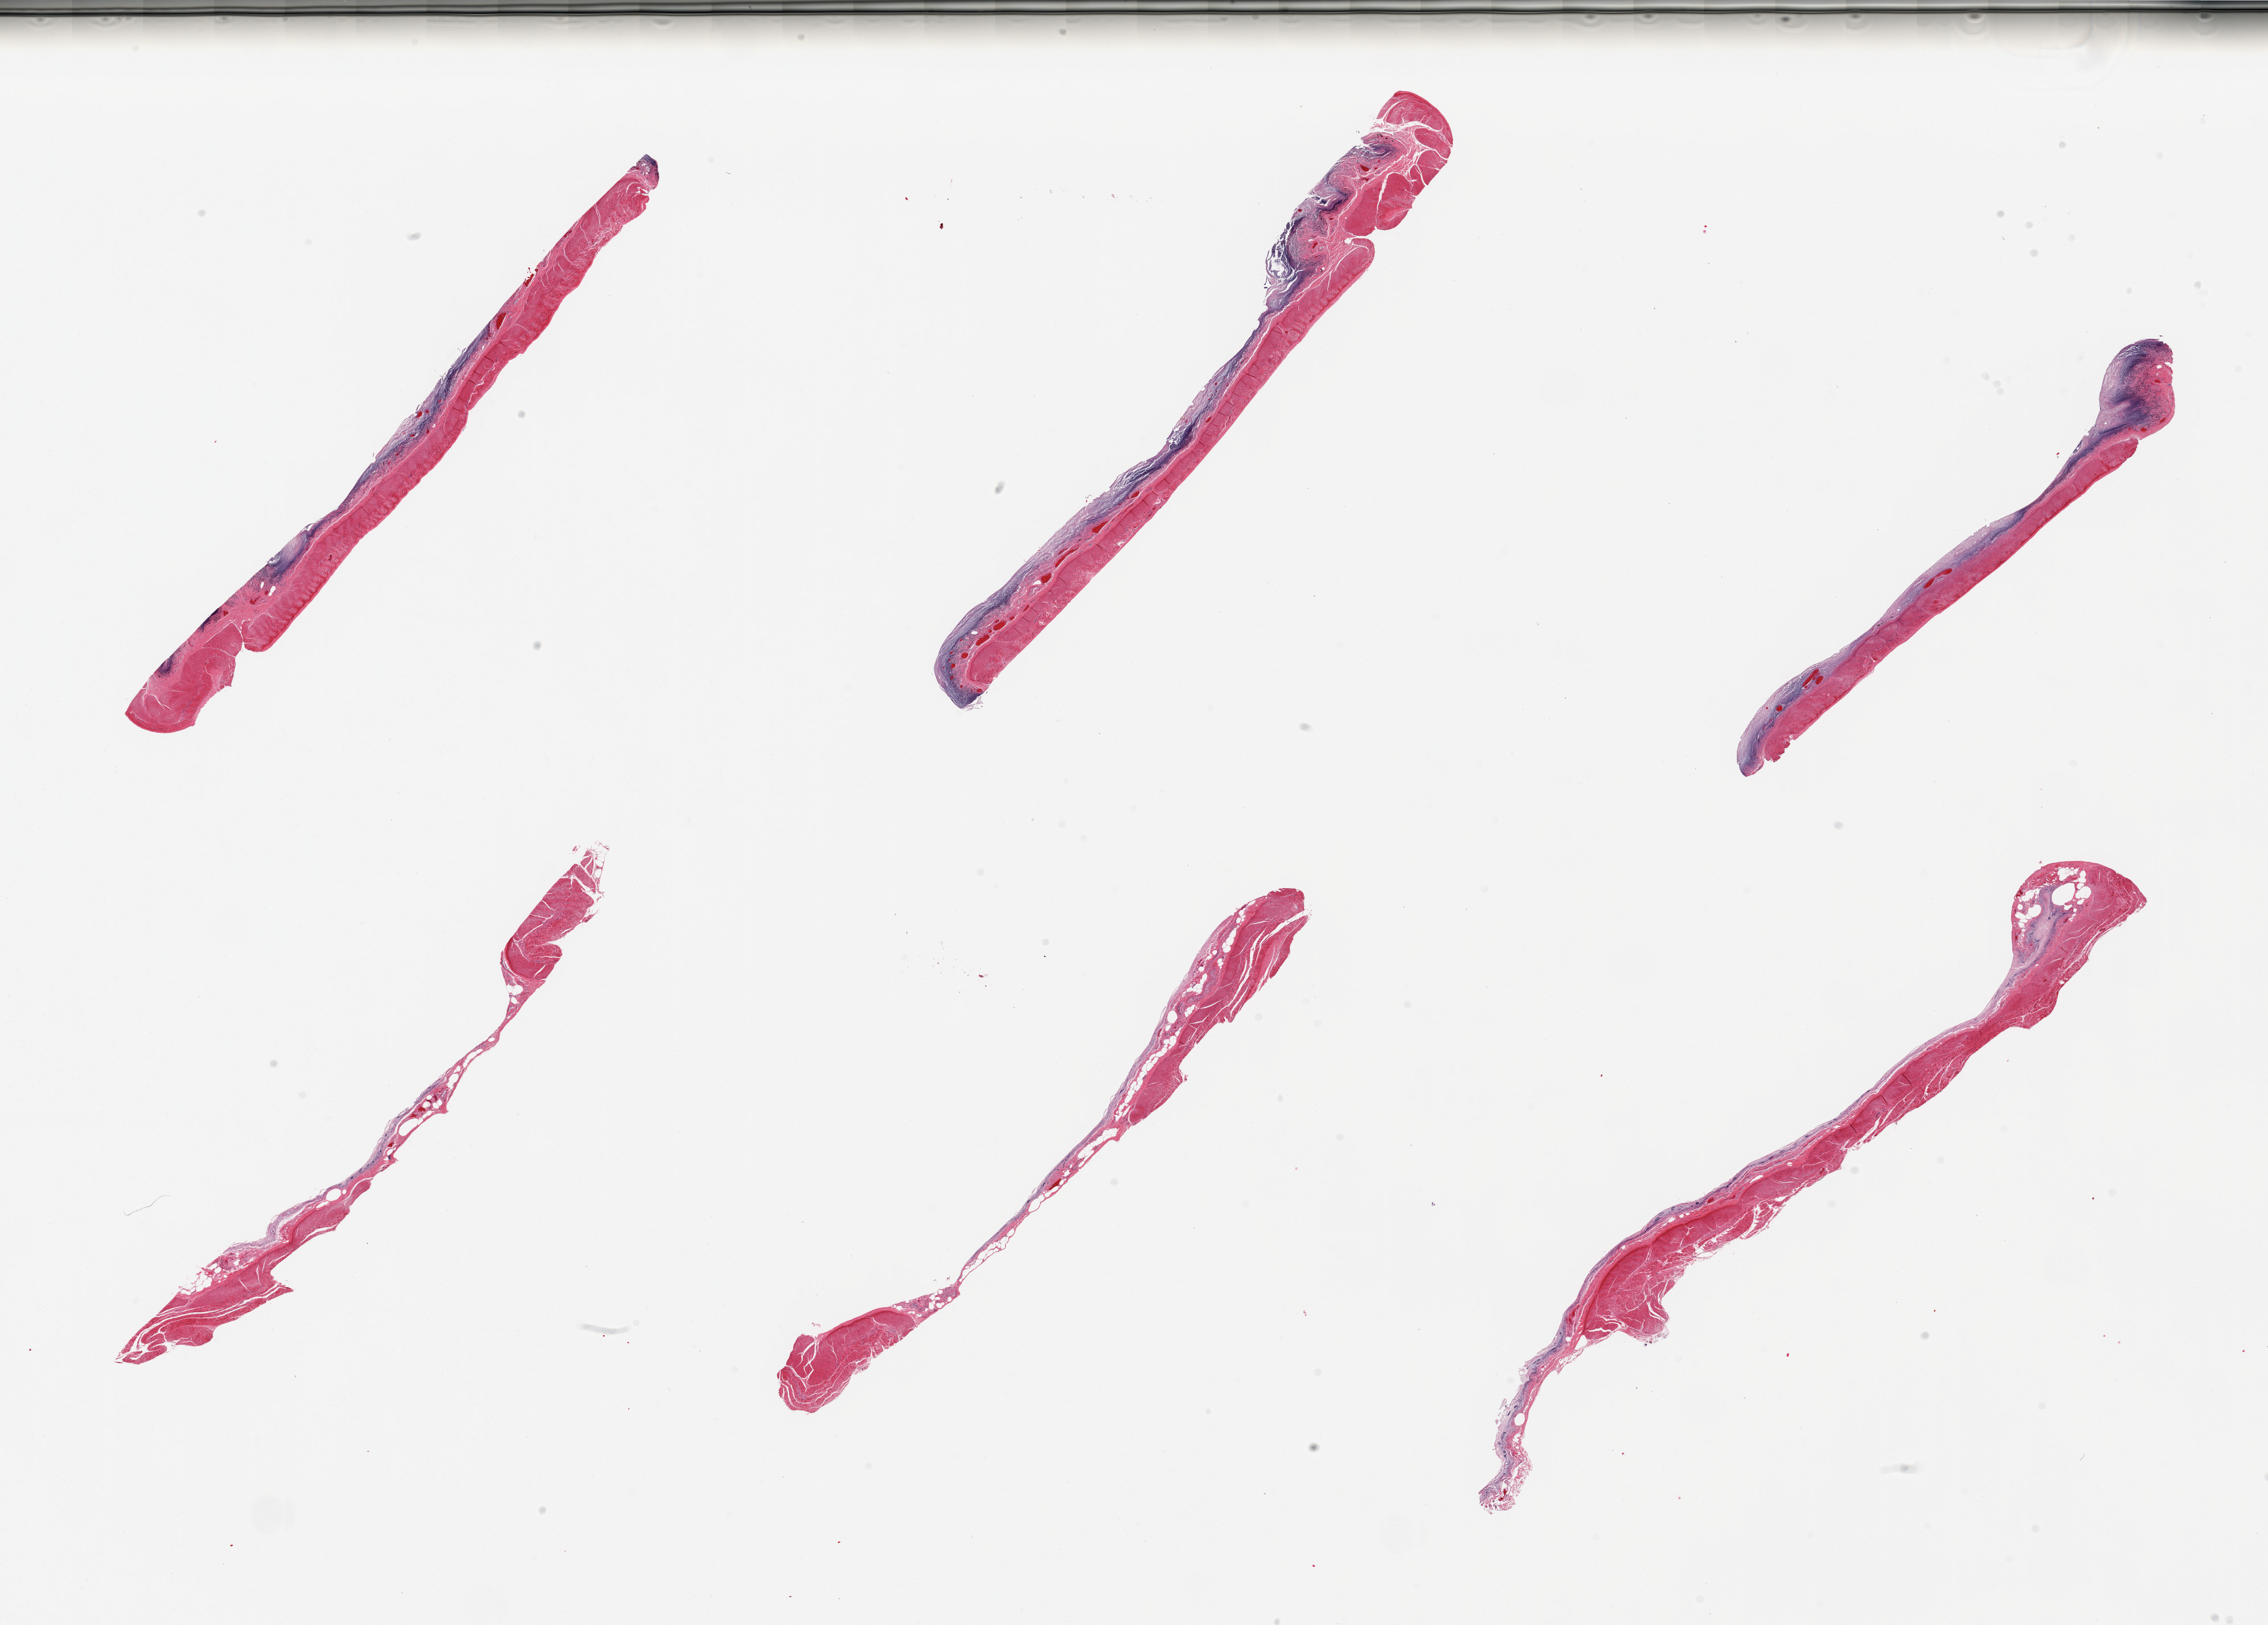
Whole-slide image, H&E stain, brightfield, low-resolution overview of the scanned area, about 31.5 x 22.6 mm (from a 20x scan), PAXgene-fixed, paraffin-embedded tissue, section of ileum (target tissue), donor tissue sample. Donor: male.
Review note (as recorded): 6 pieces; mucosal autolysis, muscularis (not target) also present.